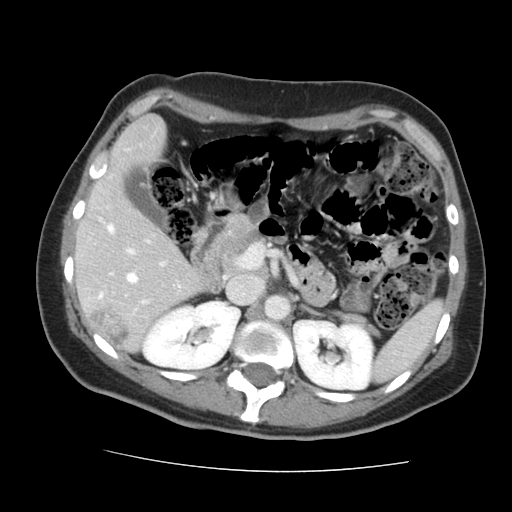
Contrast-enhanced abdominal CT, one axial slice; position 83 of 144 along the scan axis; intravenous contrast given; soft-tissue window (W 400 / L 40 HU); 2.5 mm slice thickness; 512 × 512 image matrix. Female patient, age 46 years. From the clinical record (not read from this slice): diagnosis: colorectal cancer liver metastases, imaged before liver resection; multiple liver metastases: no; largest metastasis: 2.8 cm; chemotherapy before resection: yes.
Outlined on this slice (manually delineated by an expert):
- hepatic veins: bounding box [x1, y1, x2, y2] px = [127, 273, 138, 283]
- liver: [78, 117, 202, 349]
- planned liver remnant (the part of the liver to remain after resection): [78, 117, 202, 337]
- portal vein (with intrahepatic branches): [99, 226, 166, 311]
- liver metastasis: [91, 306, 133, 347]